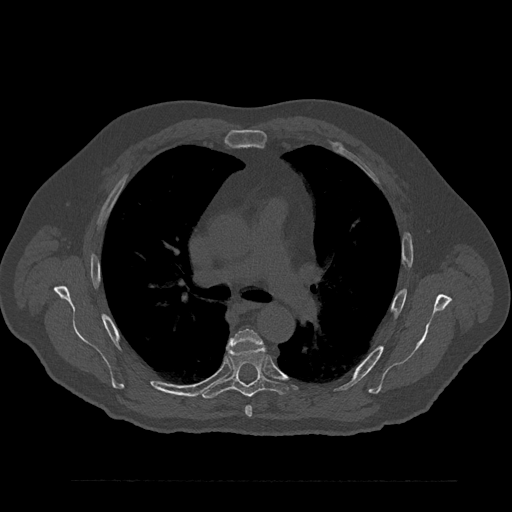
CT including the spine, one axial slice. Slice 568 of 797 in the series (ordered by position). Reconstruction kernel Br40s/3. 120 kVp. Bone window (W 1800 / L 400 HU). 0.5 mm slice thickness. 512 × 512 image matrix, field of view 430 × 430 mm. Male patient, age 61 years. Case-level facts recorded for this patient, not image findings: primary cancer: prostate.
Outlined on this slice (semi-automatic segmentation, software-assisted and operator-edited):
- T5 vertebra: bounding box <230,328,262,417> (left, top, right, bottom; pixels)
- T6 vertebra: <201,346,288,399>